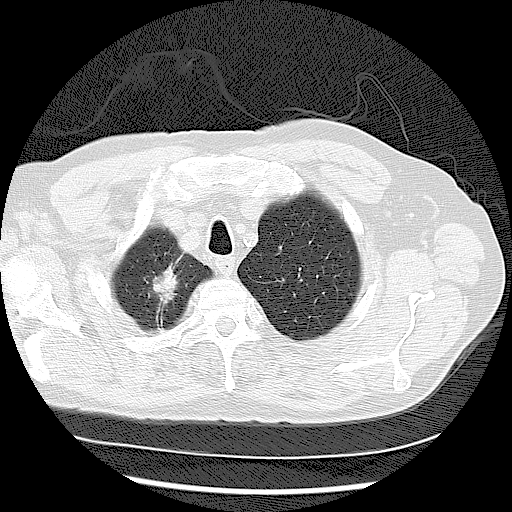
Low-dose screening chest CT, one axial slice; slice 102 of 122 in the series (ordered by position); reconstruction kernel LUNG; 120 kVp; lung window (W 1500 / L -600 HU); 2.5 mm slice thickness; 512 × 512 image matrix, field of view 360 × 360 mm.
Outlined on this slice (outlined manually by an expert reader):
- lesion 2 (tumor, upper lobe of right lung): bounding box <153,263,178,306> (left, top, right, bottom; pixels)